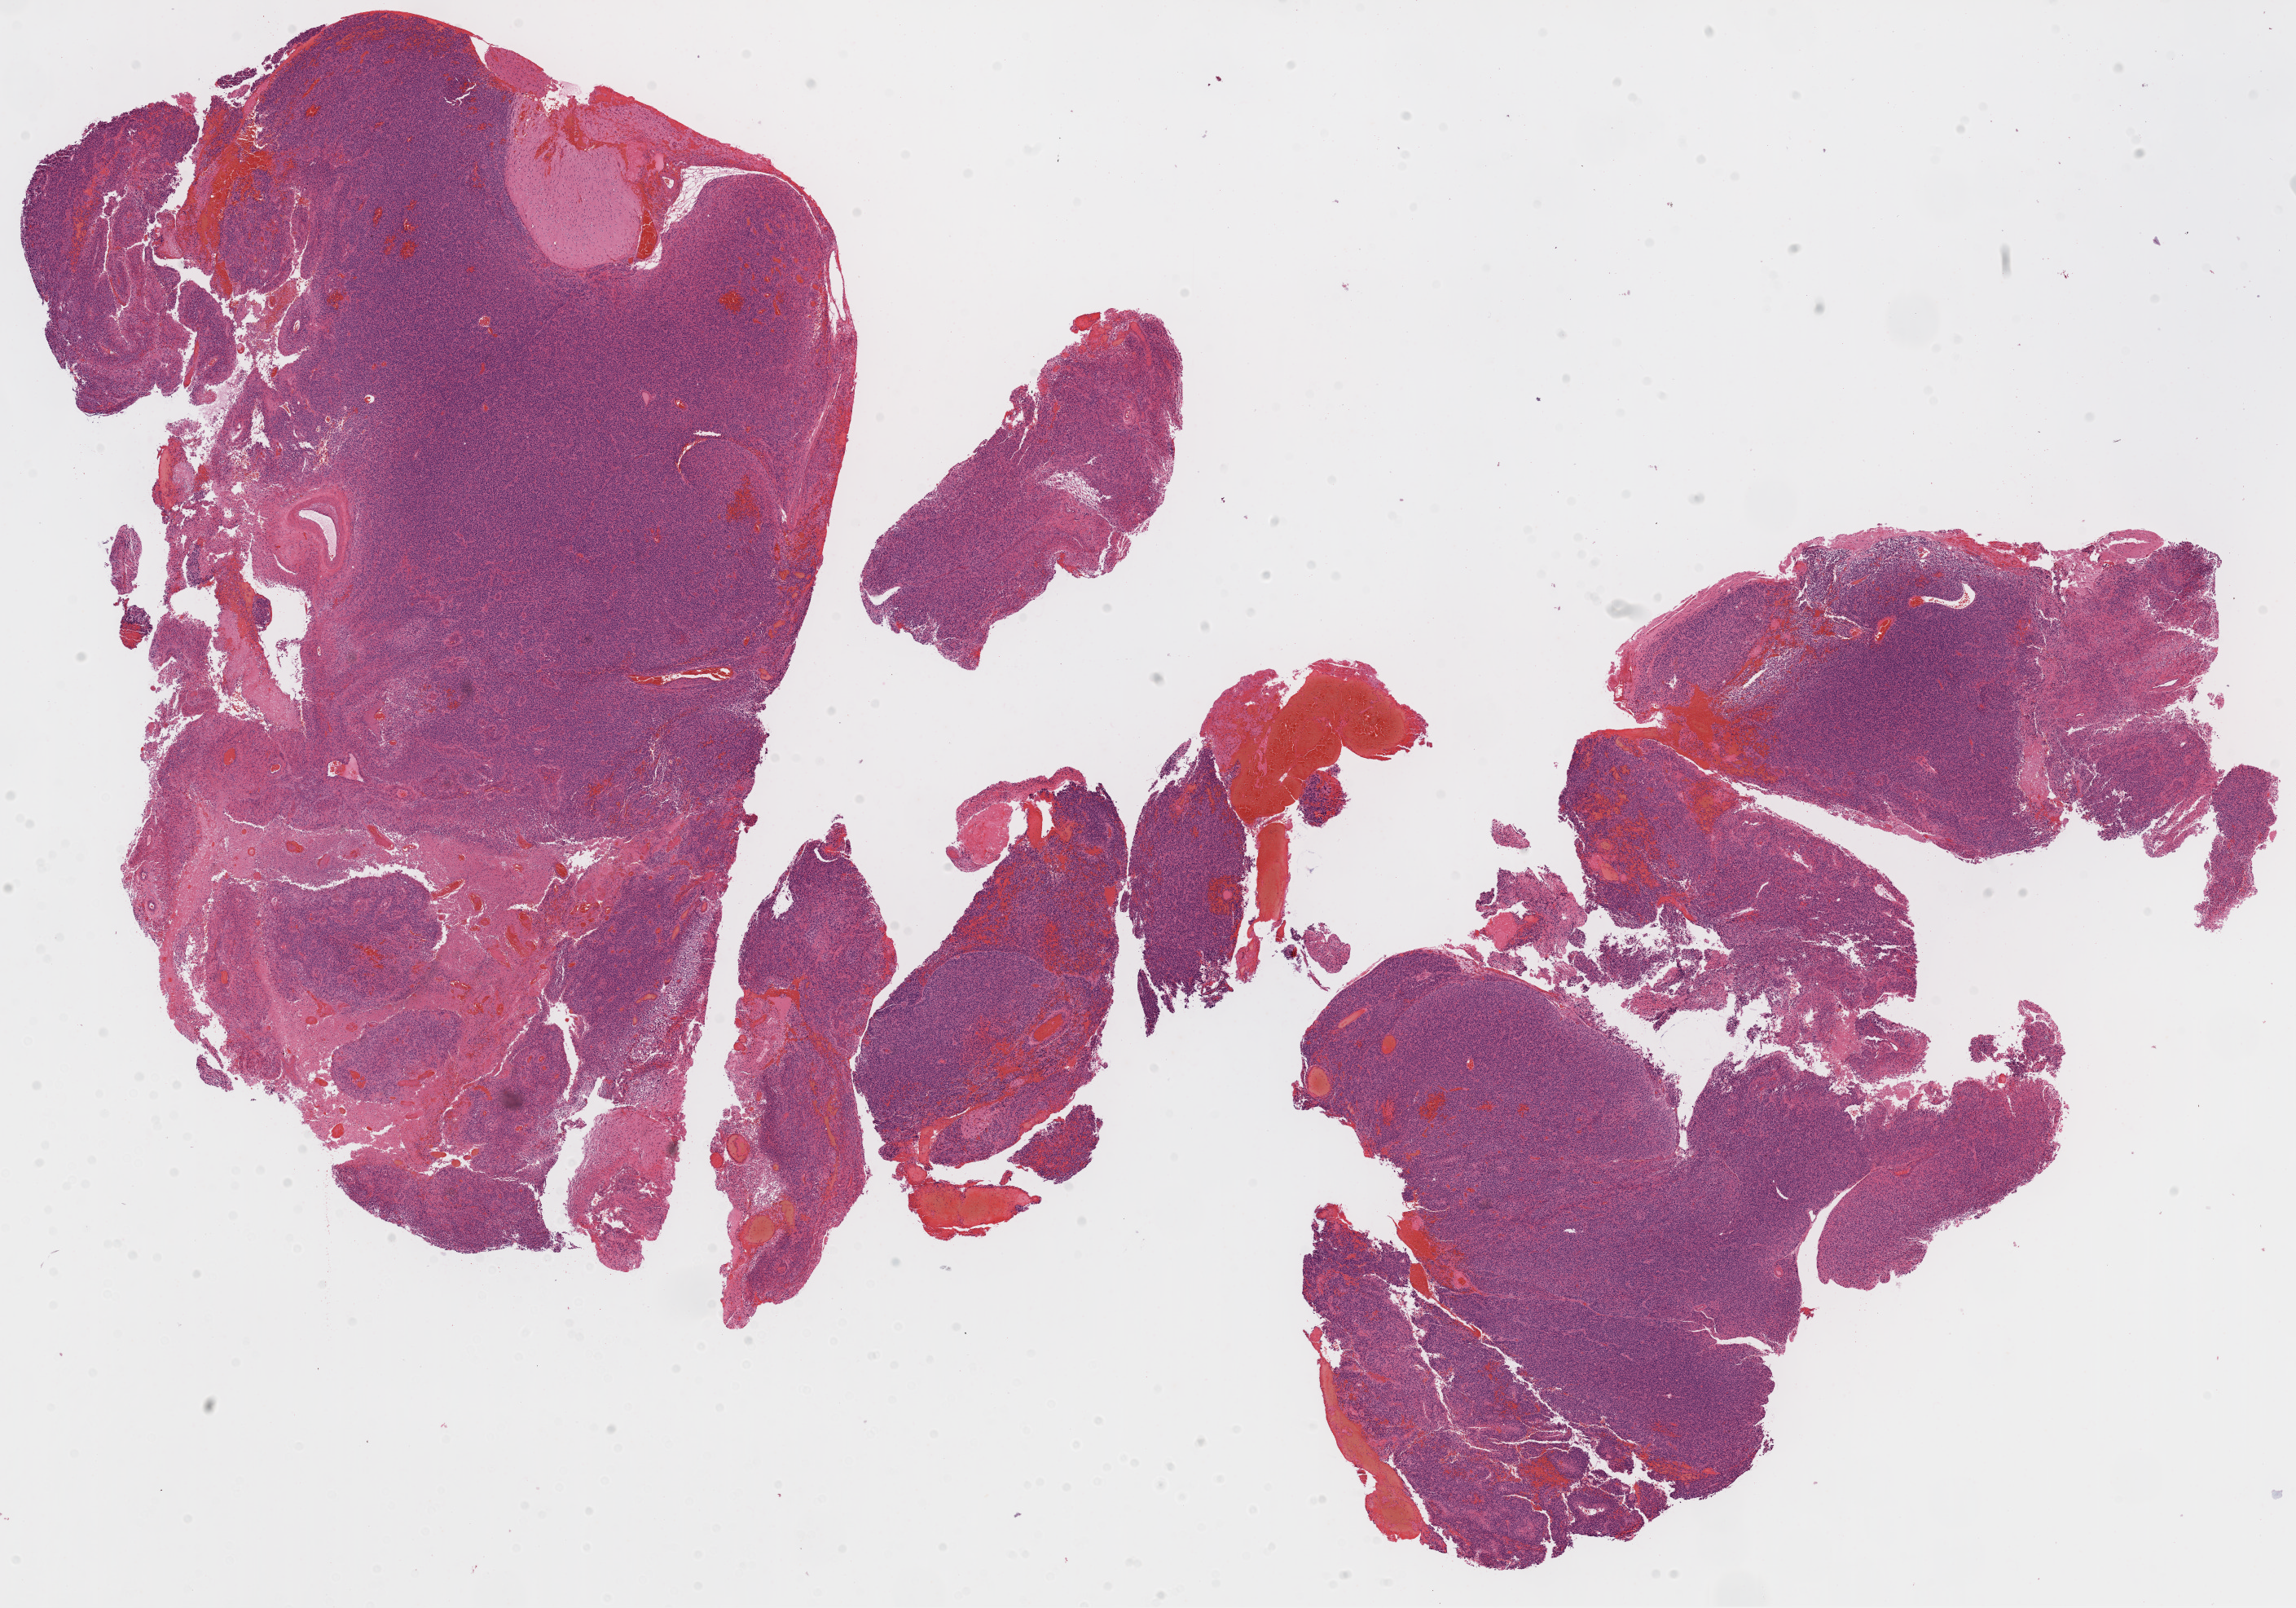
Whole-slide histology image, H&E, whole scanned area (about 22.7 x 15.9 mm, from a 20x scan) shown as a low-resolution overview; formalin-fixed paraffin-embedded (FFPE) diagnostic section; sample: primary tumour, brain. Female patient; age at initial diagnosis 61 years.
• histologic diagnosis: Glioblastoma